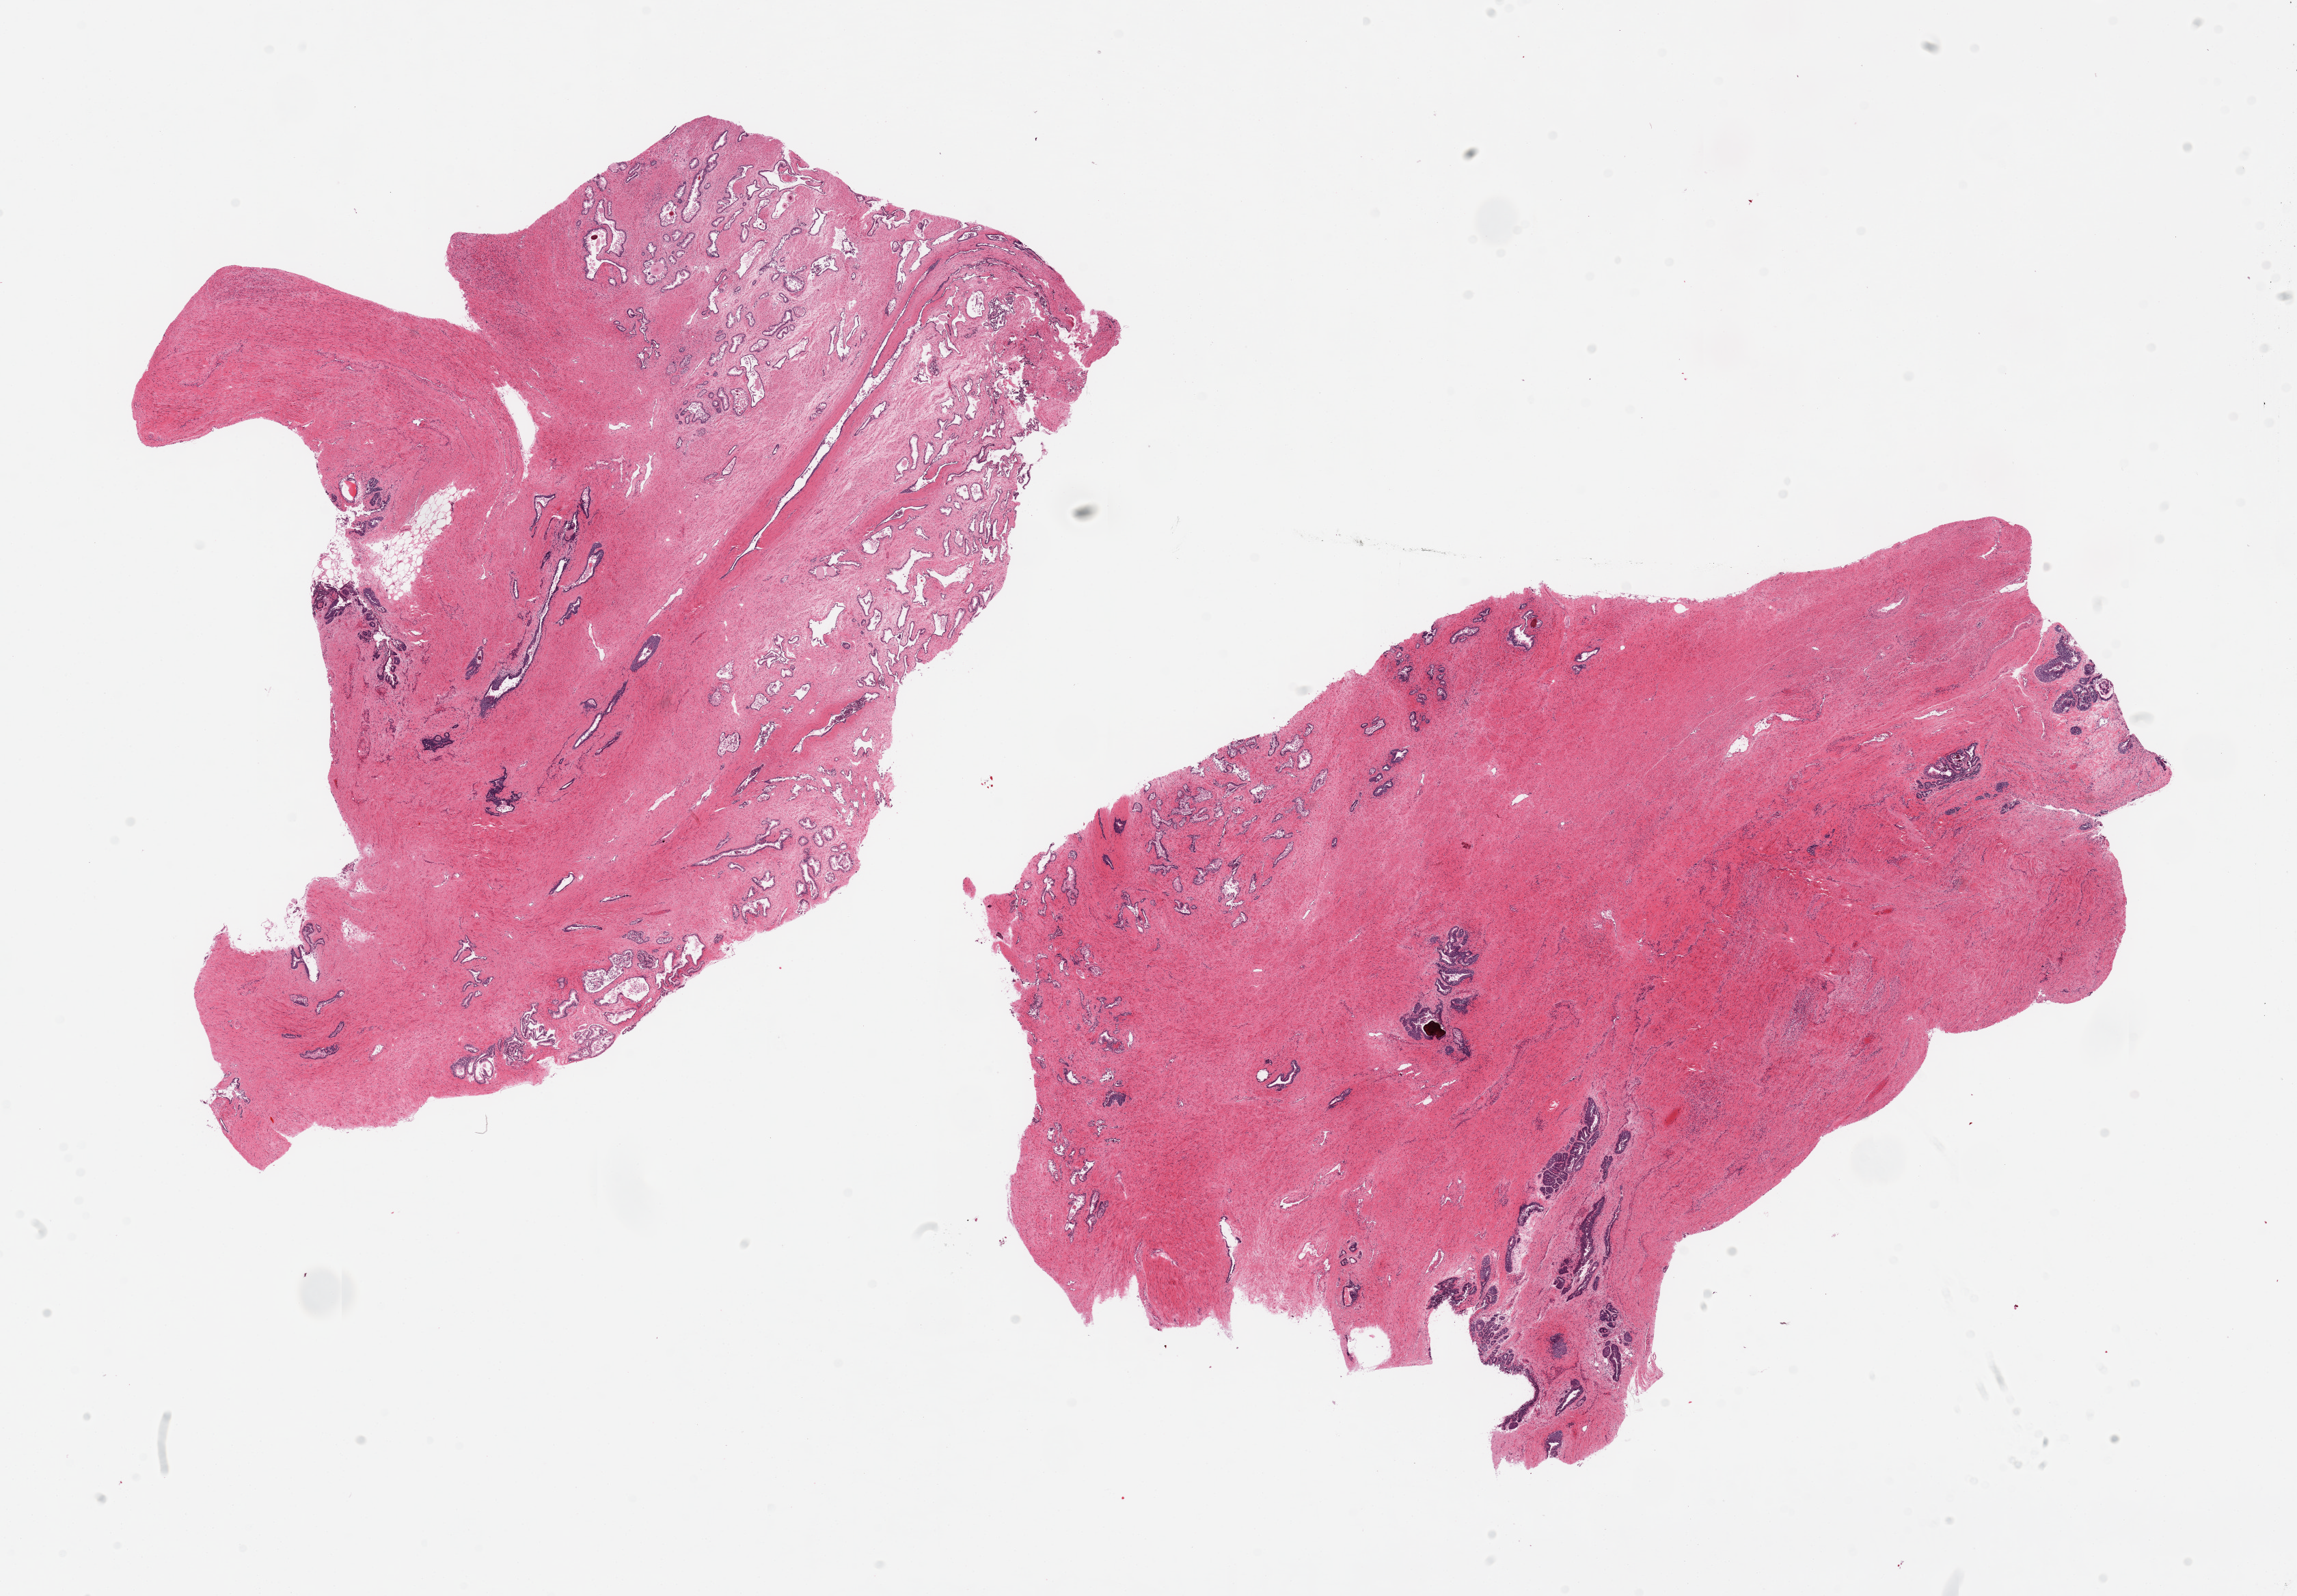
Whole-slide image, hematoxylin and eosin (H&E) stain, brightfield — whole scanned area (about 26.6 x 18.5 mm, from a 20x scan) shown as a low-resolution overview, PAXgene-fixed paraffin-embedded (PFPE) section, target tissue: prostate, donor tissue sample. Donor: male.
Reviewer comment on this tissue sample: 2 pieces, atrophic appearing glands. Focally moderate autolysis (2).